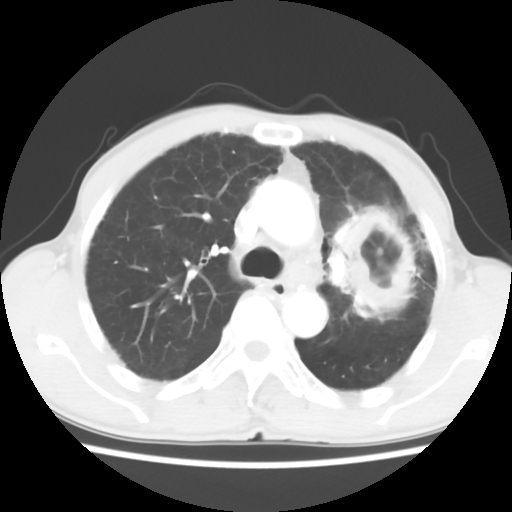
Chest CT, one axial slice. Slice 41 of 60 in the series (ordered by position). Reconstruction kernel STANDARD. 120 kVp. Lung window (W 1500 / L -600 HU). 5 mm slice thickness. 512 × 512 image matrix. Male patient, age 64 years. From the clinical record (not read from this slice): clinical TNM (as recorded): T3 N3 M0; histopathological grade: G3.
Annotated regions visible in this slice (bounding box drawn by a radiologist):
- lung tumour (recorded histology: adenocarcinoma): bounding box (x1, y1, x2, y2) in pixels: (326, 189, 441, 345)